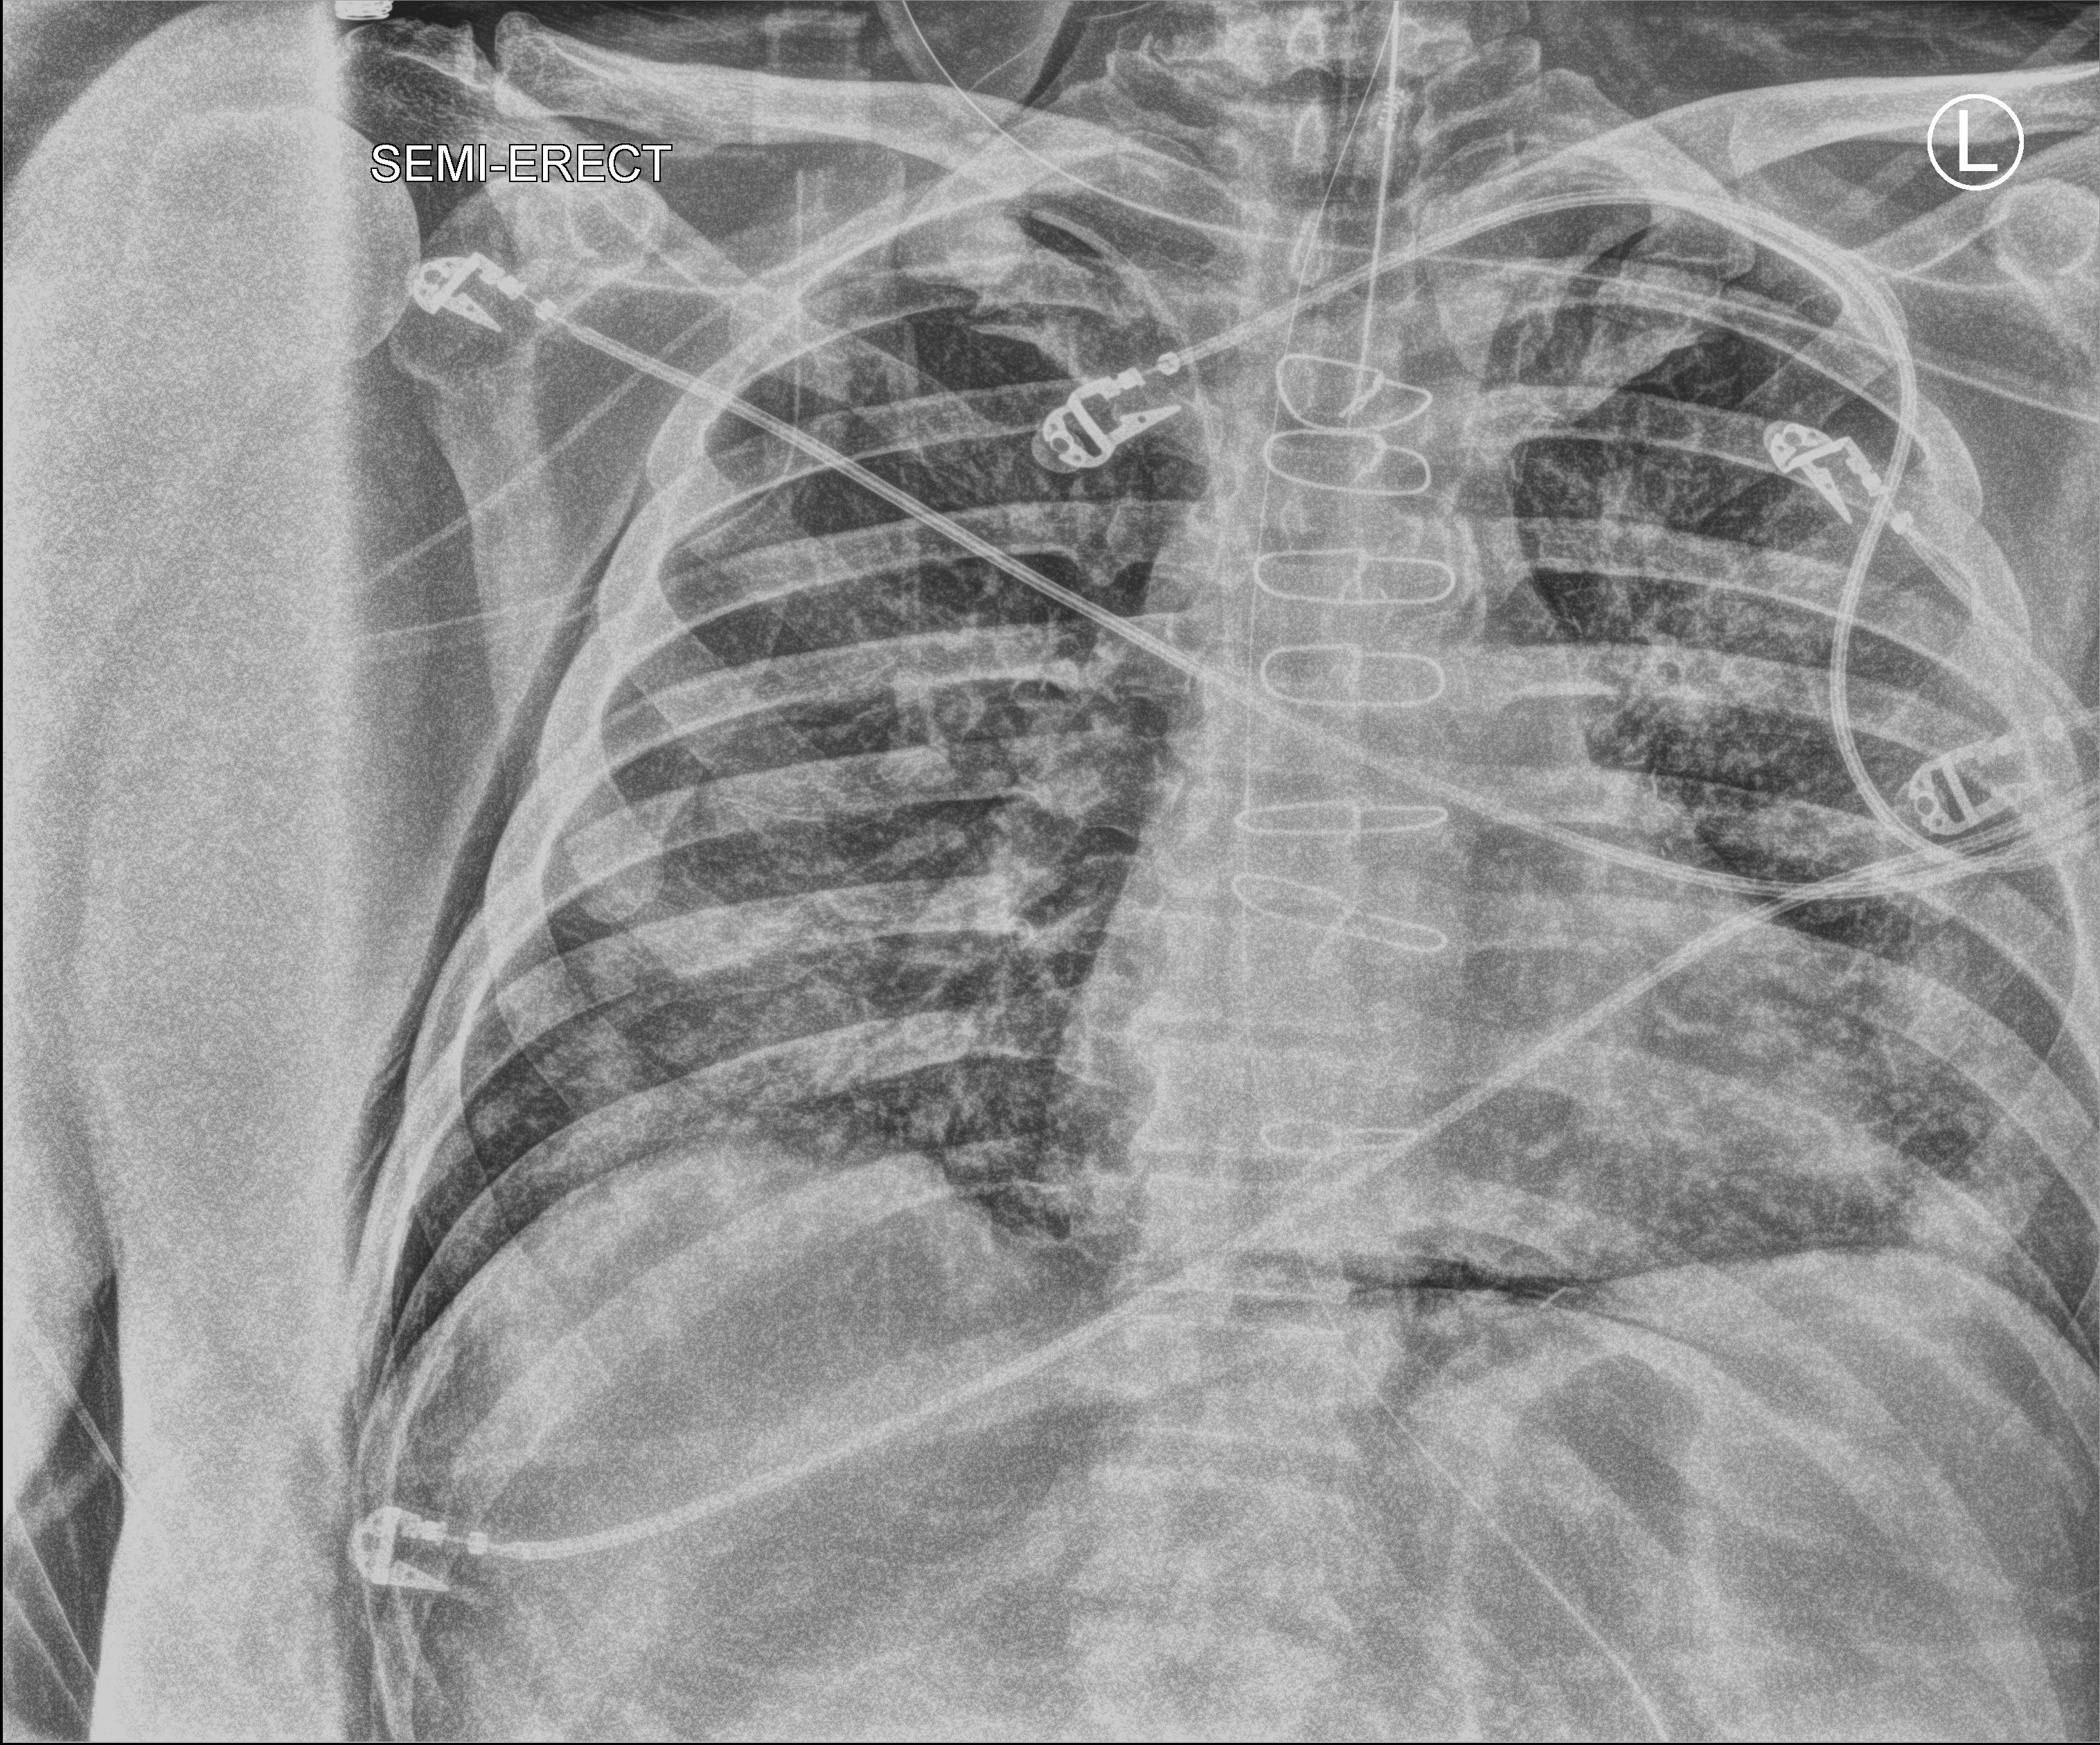
Portable chest radiograph, anteroposterior (AP) projection. Male patient hospitalised with COVID-19, age 60–74 years.
From the hospital-stay record, not from the radiograph (when in the stay this image was taken is not recorded): admitted to intensive care during this hospital stay: yes; mechanically ventilated during this hospital stay: yes; COPD (admission record): no.